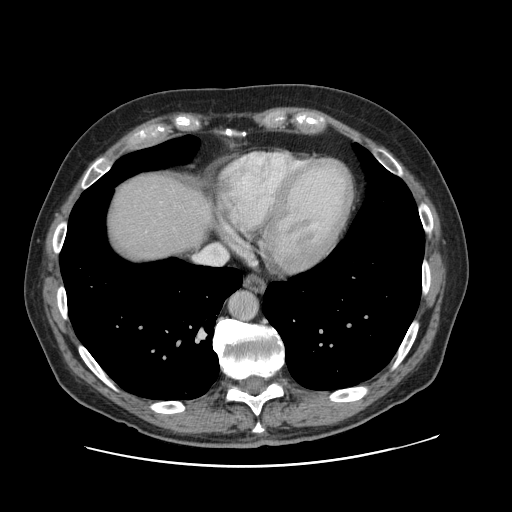
Contrast-enhanced abdominal CT, one axial slice. Position 112 of 138 along the scan axis. 120 kVp. Intravenous contrast given. Soft-tissue window (W 400 / L 40 HU). 512 × 512 image matrix, field of view 402 × 402 mm. Male patient, age 71 years. From the clinical record (not read from this slice): diagnosis: colorectal cancer liver metastases, imaged before liver resection; multiple liver metastases: no; largest metastasis: 3.3 cm.
Structures marked on this image (expert manual segmentation):
- hepatic veins: bounding box <197,244,228,267> (left, top, right, bottom; pixels)
- liver: <106,171,214,264>
- planned liver remnant (the part of the liver to remain after resection): <106,172,209,264>